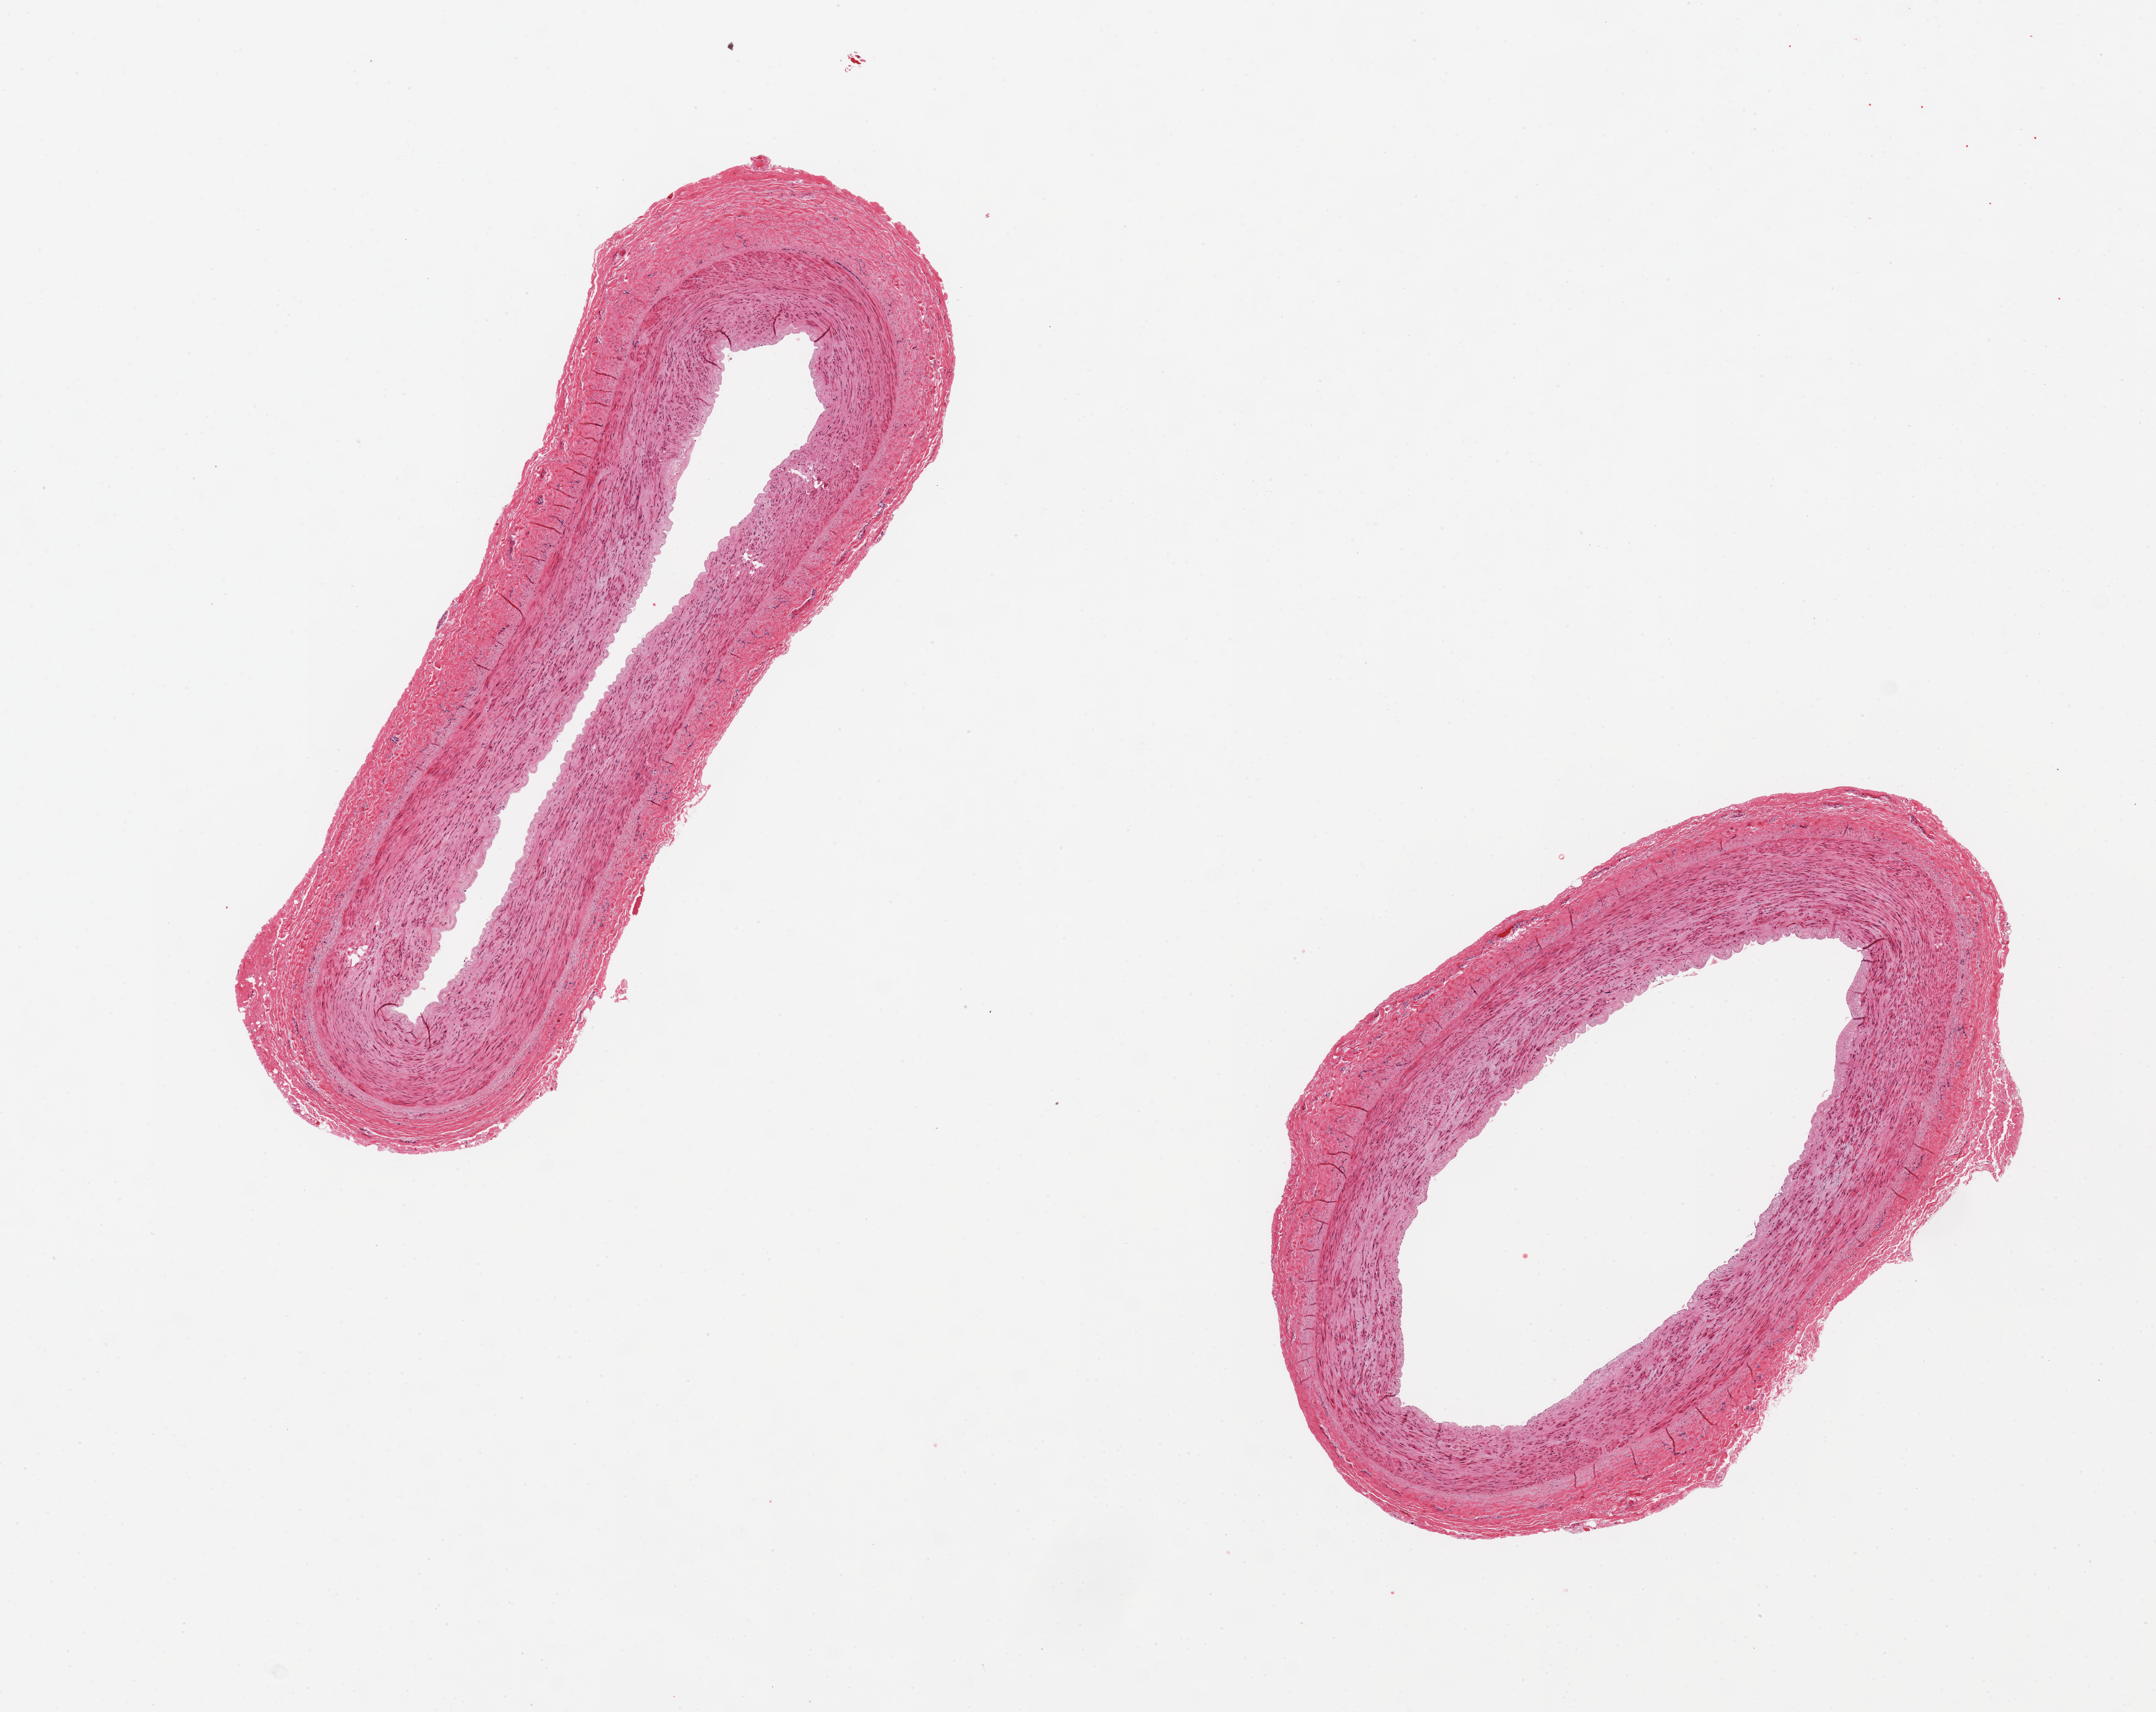
Digitized haematoxylin and eosin-stained section — shown as a low-resolution overview of the whole scanned area (about 13.8 x 10.9 mm, from a 20x scan); PAXgene-fixed, paraffin-embedded tissue; sampled site (target tissue): tibial artery; tissue donor sample.
Reviewer comment on this tissue sample: 2 pieces, ~6 mm artery; no sclerosis; no external adipose [good clean vessel].